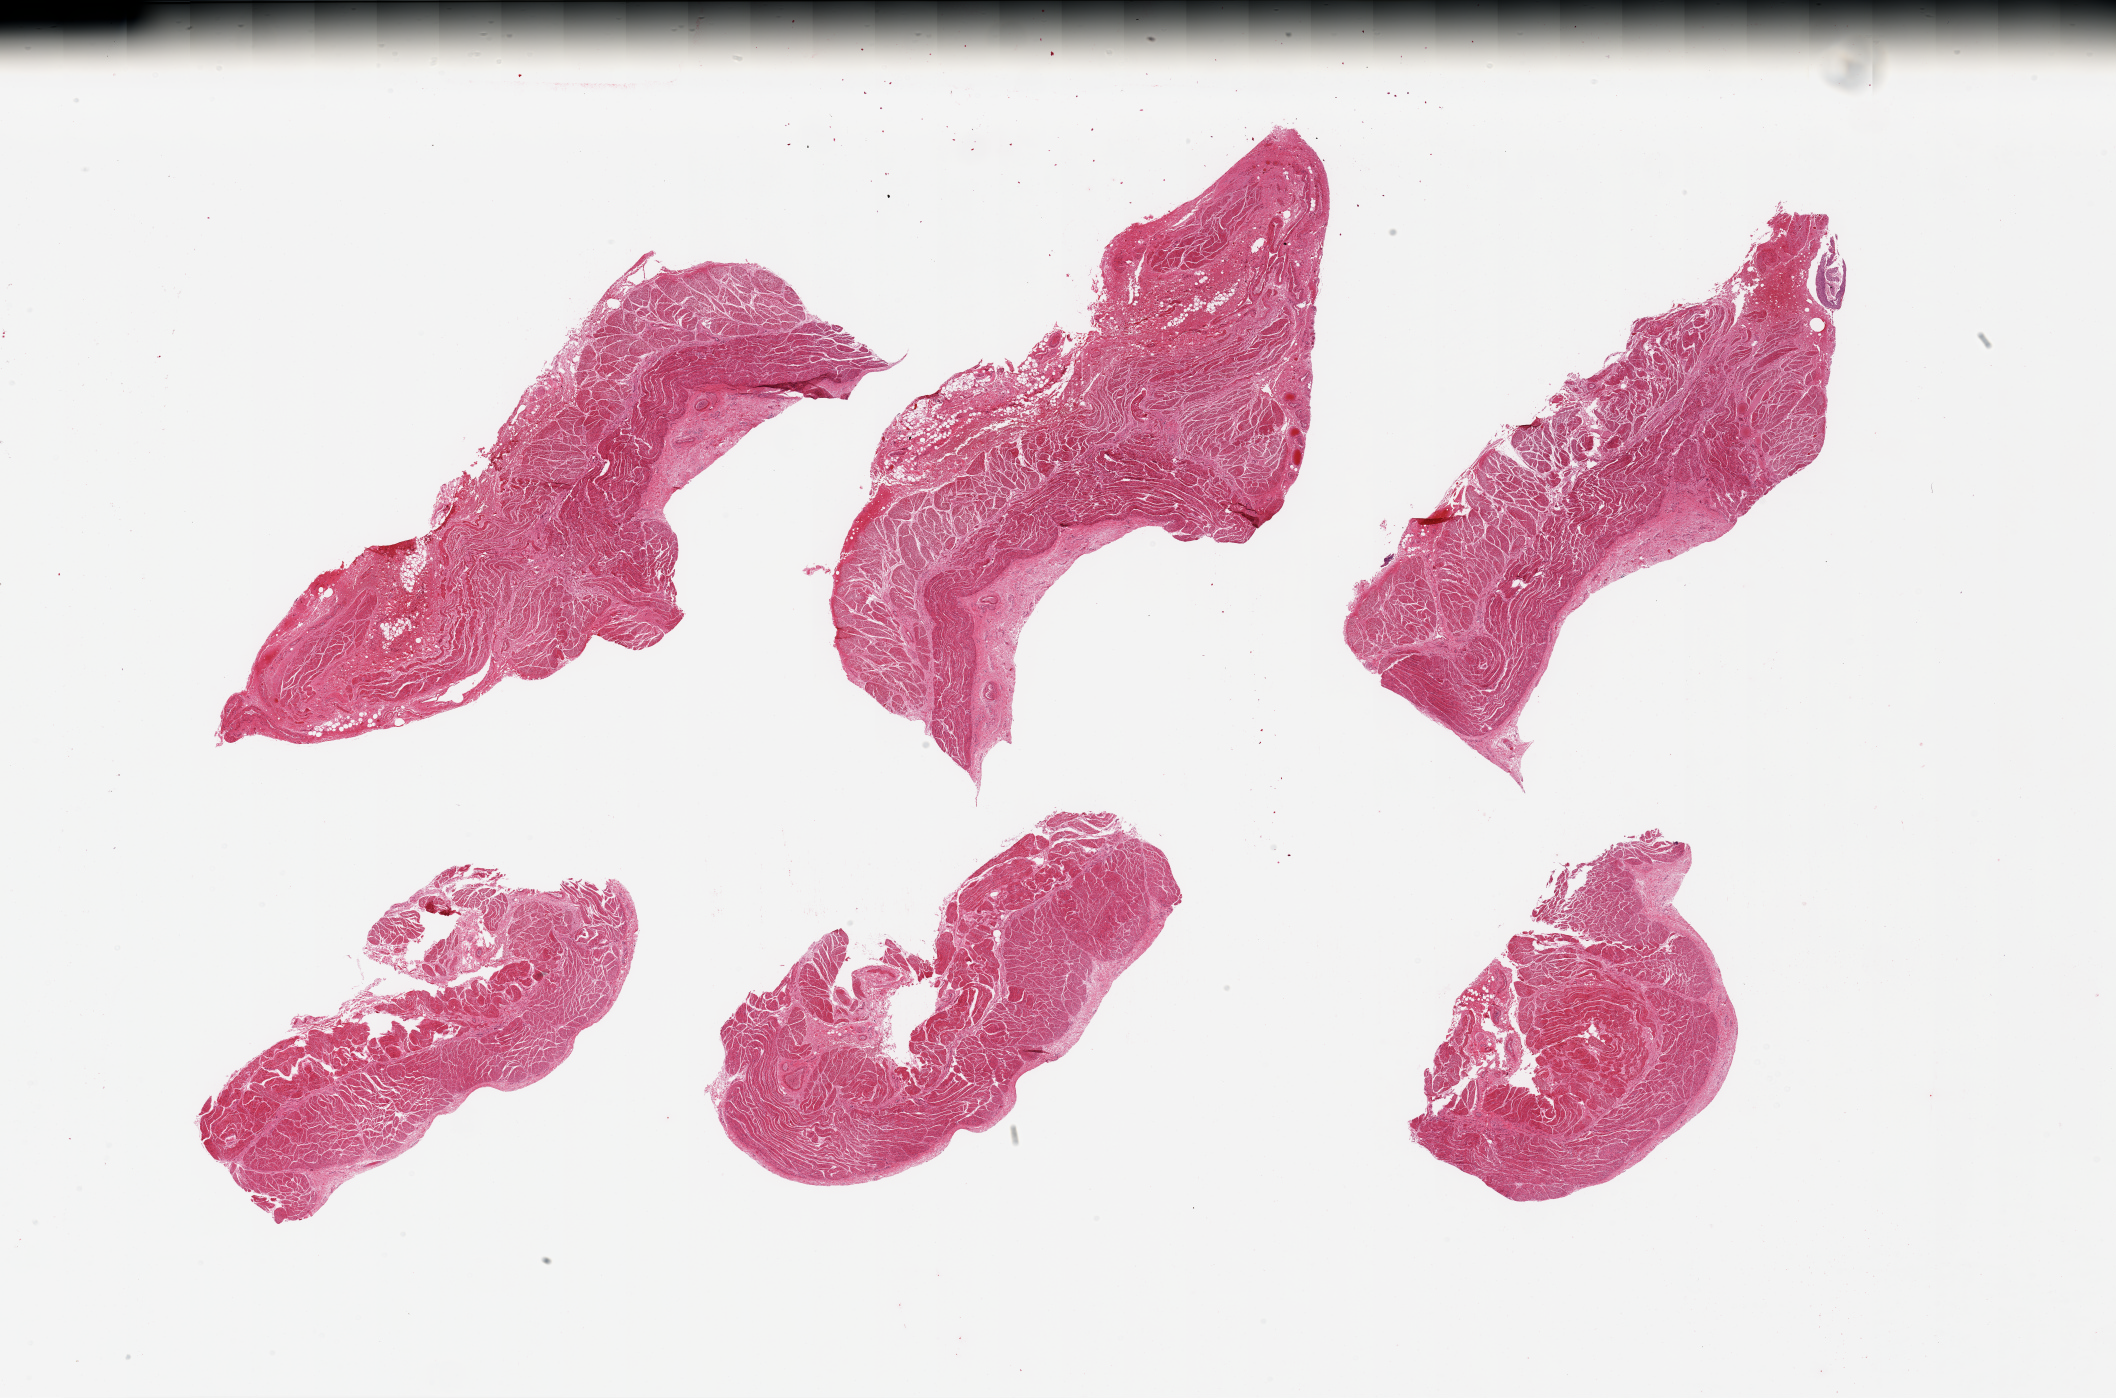
Digitized haematoxylin and eosin-stained section, brightfield, low-resolution overview of the scanned area, about 33.5 x 22.1 mm; PAXgene-fixed, paraffin-embedded tissue; target tissue: esophageal muscle; donor tissue sample. Donor: male.
* reviewer comment on this tissue sample: 6 pieces; well dissected